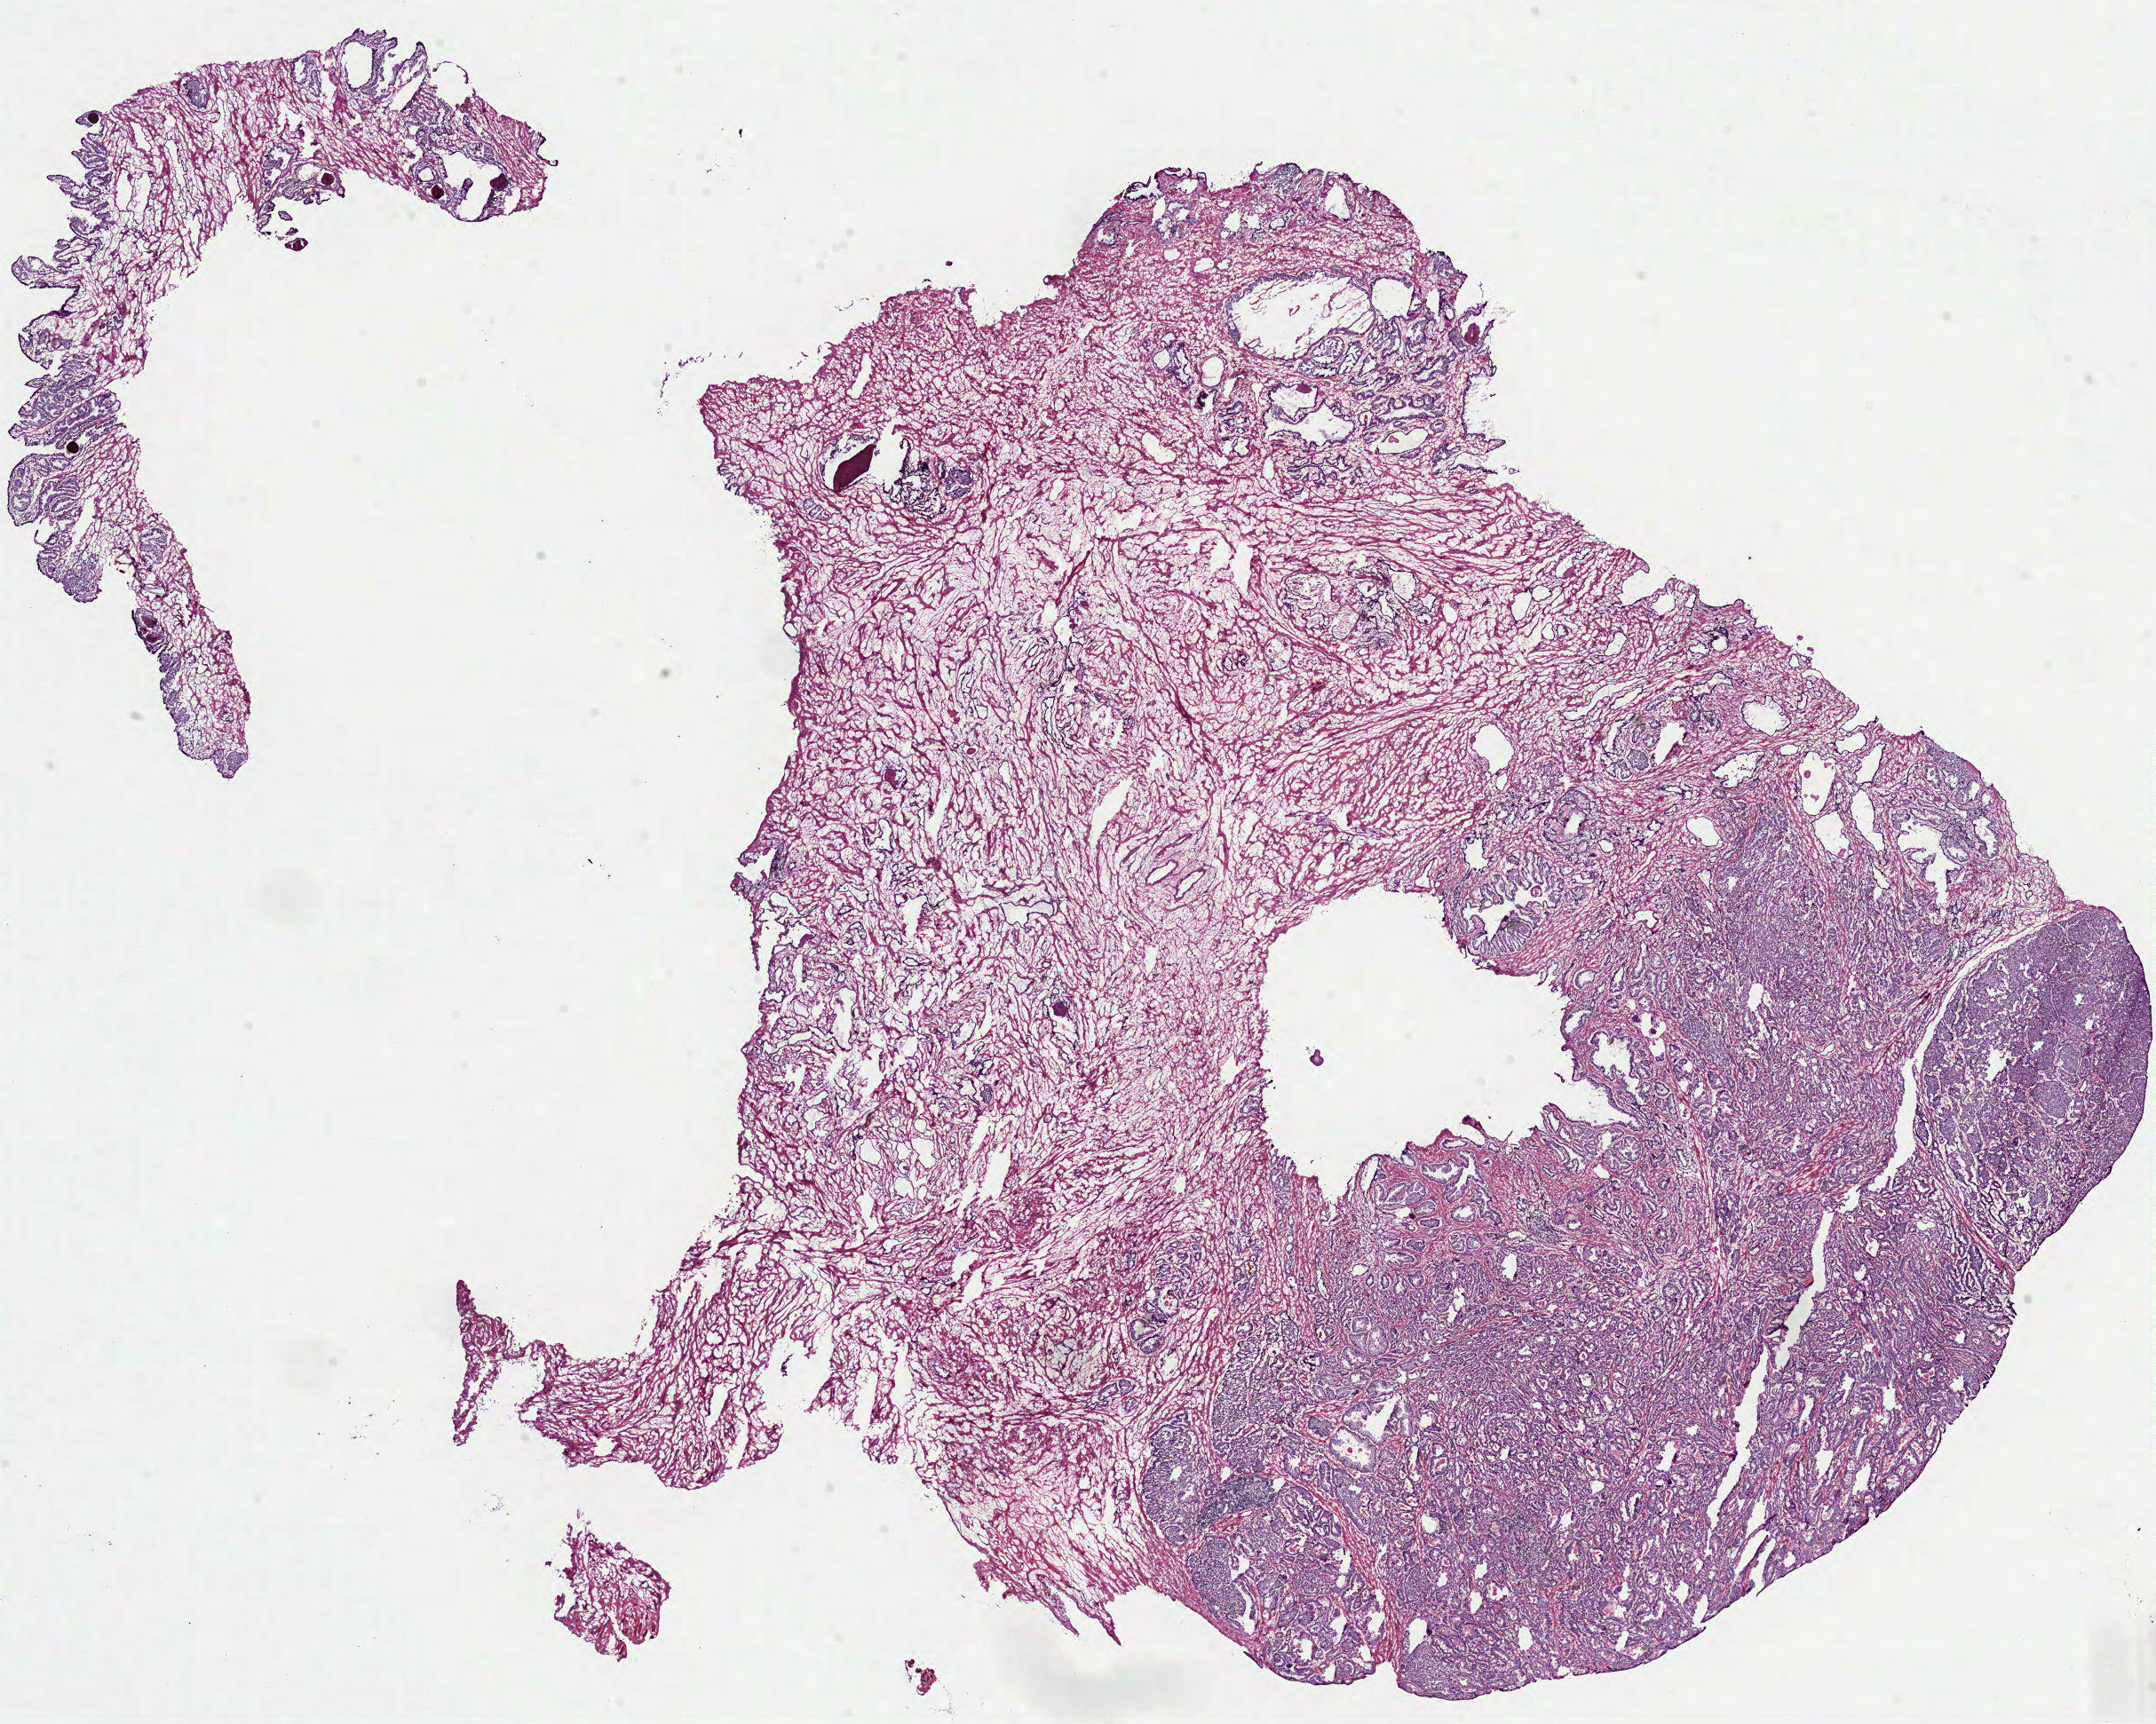
Digitized H&E tissue section (whole slide), shown as a low-resolution overview of the whole scanned area (about 19.6 x 15.7 mm); frozen section; primary tumour sample from the prostate. Patient: male, age at initial diagnosis 64 years. Gleason score: 7 (3+4). Composition of this section per pathologist review: tumour cells 80%, tumour nuclei 75%, normal cells 10%, stromal cells 10%, necrosis 0%. Infiltration values recorded for this section: lymphocyte infiltration 2%, monocyte infiltration 0%, neutrophil infiltration 0%.
Diagnosis: Acinar cell carcinoma (prostate gland). Lymph nodes positive (case pathology): 0 of 7 examined. Laterality: bilateral.